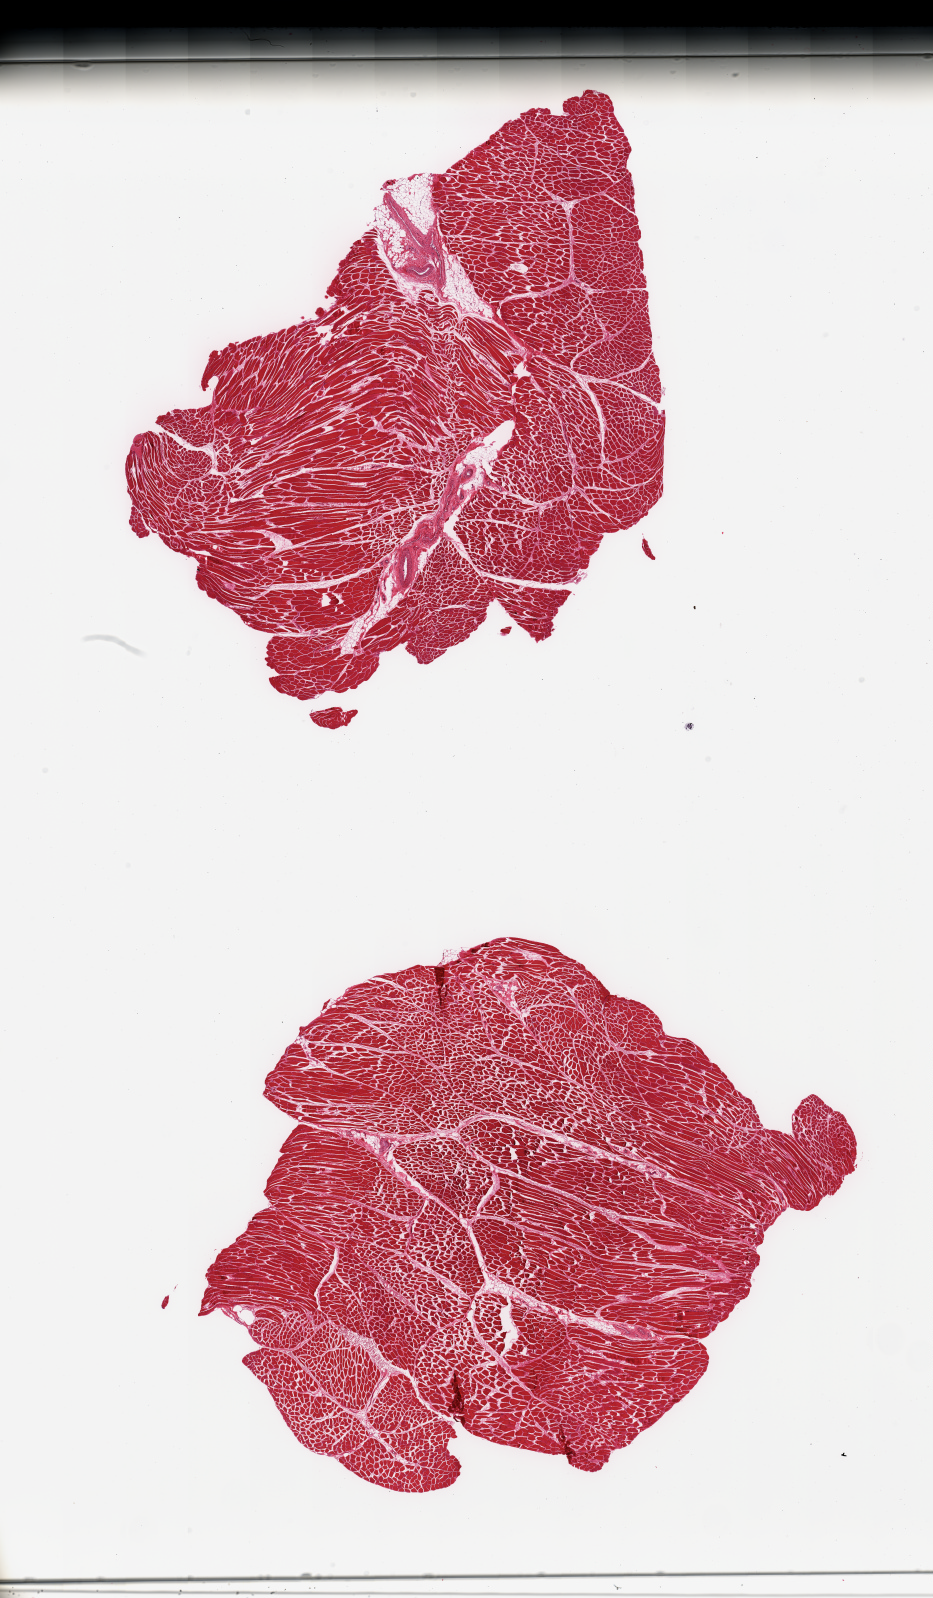
Digitized H&E-stained section — whole scanned area (about 14.8 x 25.3 mm, from a 20x scan) shown as a low-resolution overview. PAXgene-fixed paraffin-embedded (PFPE) section. Sampled site (target tissue): skeletal muscle. Tissue donor sample. Donor: male.
Pathologist's review note for this sample: 2 pieces; <5% fat content.